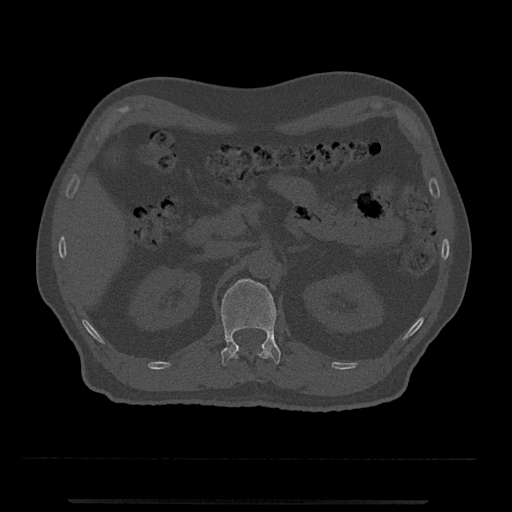
CT including the spine, one axial slice; position 355 of 797 along the scan axis; reconstruction kernel Br40s/3; 120 kVp; bone window (W 1800 / L 400 HU); 0.5 mm slice thickness; 512 × 512 image matrix. Patient: male, 63 years. Case-level facts recorded for this patient, not image findings: primary cancer: prostate.
Annotated regions visible in this slice (semi-automatically segmented with operator editing):
- L1 vertebra: bounding box <221,278,281,366> (left, top, right, bottom; pixels)
- T12 vertebra: <231,346,270,359>